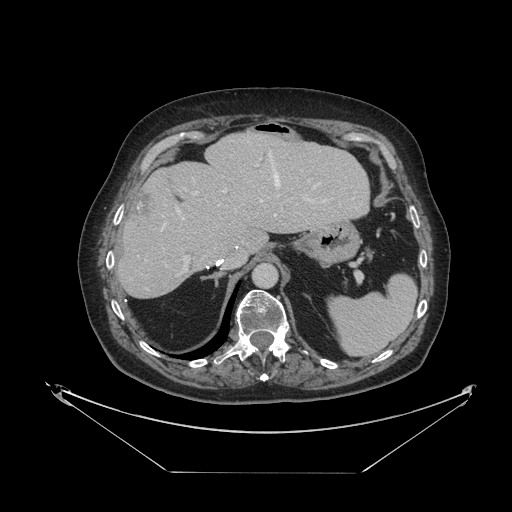
Contrast-enhanced abdominal CT, one axial slice. Slice 75 of 121 in the series (ordered by position). Reconstruction kernel STANDARD. Intravenous contrast given. Soft-tissue window (W 400 / L 40 HU). 2.5 mm slice thickness. 512 × 512 image matrix, field of view 500 × 500 mm. Male patient, age 68 years. Case-level facts recorded for this patient, not image findings: diagnosis: colorectal cancer liver metastases, imaged before liver resection; multiple liver metastases: no; largest metastasis: 4 cm; disease in both lobes: no.
Outlined on this slice (outlined manually by an expert reader):
- hepatic veins: box from (x=161, y=152) to (x=320, y=231) px
- liver: (x=119, y=134)–(x=369, y=298)
- planned liver remnant (the part of the liver to remain after resection): (x=119, y=134)–(x=369, y=298)
- portal vein (with intrahepatic branches): (x=180, y=164)–(x=312, y=274)
- liver metastasis: (x=132, y=192)–(x=153, y=219)